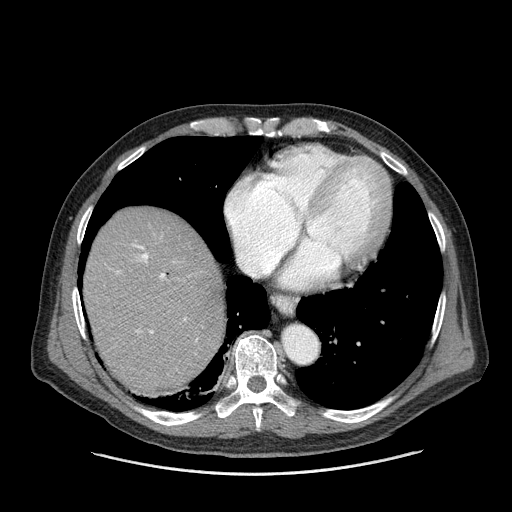
Contrast-enhanced abdominal CT (liver protocol), one axial slice; slice 136 of 180 in the series (ordered by position); one of 2 acquisitions stored at this slice position; soft-tissue window (W 400 / L 40 HU); 2.5 mm slice thickness; 512 × 512 image matrix. From the clinical record (not read from this slice): diagnosis: hepatocellular carcinoma (patient treated with transarterial chemoembolisation; whether this scan precedes or follows treatment is not stated here); TNM stage (as recorded): Stage-II; Child-Pugh class: A.
Outlined on this slice (semi-automatic segmentation, software-assisted and operator-edited):
- abdominal aorta: bounding box [x1, y1, x2, y2] px = [283, 326, 318, 362]
- liver parenchyma outside the tumour (the mass and vessels are separate outlines, so this box may not span the whole liver): [84, 206, 224, 396]
- liver vessels: [132, 244, 197, 341]